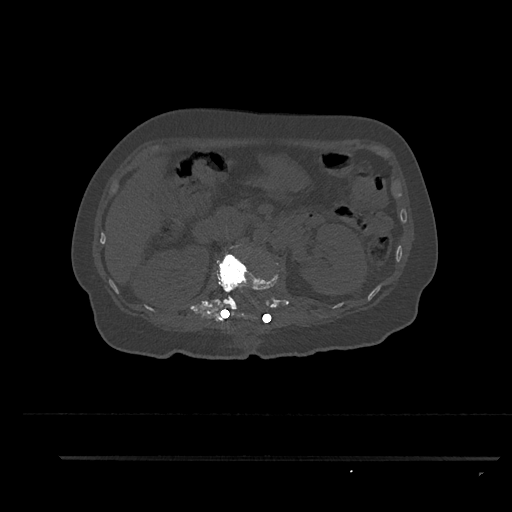
CT including the spine, one axial slice. Position 202 of 797 along the scan axis. 120 kVp. Bone window (W 1800 / L 400 HU). 512 × 512 image matrix, field of view 408 × 408 mm. Patient: female, 44 years. Case-level facts recorded for this patient, not image findings: primary cancer: renal; vertebrae with lytic lesions (as recorded): L1.
Outlined on this slice (semi-automatically segmented with operator editing):
- L1 vertebra: bounding box (x1, y1, x2, y2) in pixels: (216, 244, 279, 319)